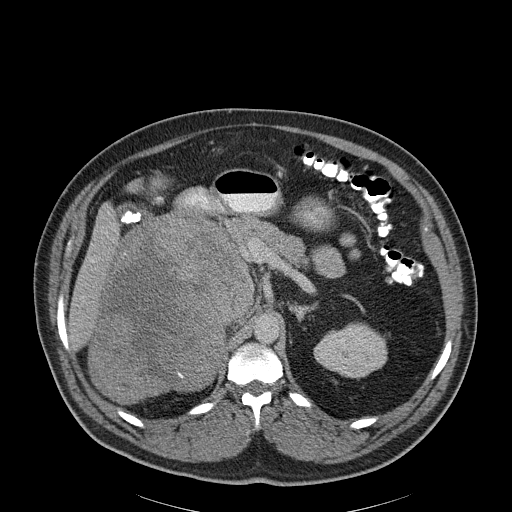
Contrast-enhanced abdominal CT, one axial slice; slice 130 of 186 in the series (ordered by position); reconstruction kernel B30f; 120 kVp; soft-tissue window (W 400 / L 40 HU); 3 mm slice thickness; 512 × 512 image matrix, field of view 464 × 464 mm. Male patient, age 56 years. From the clinical record (not read from this slice): diagnosis: adrenocortical carcinoma; tumour side: right adrenal; tumour size at pathology: 18 cm; Ki-67 index: 2 %; stage (as recorded): 3.
Structures marked on this image (semi-automatic segmentation, software-assisted and operator-edited):
- mass: box from (x=92, y=214) to (x=251, y=400) px